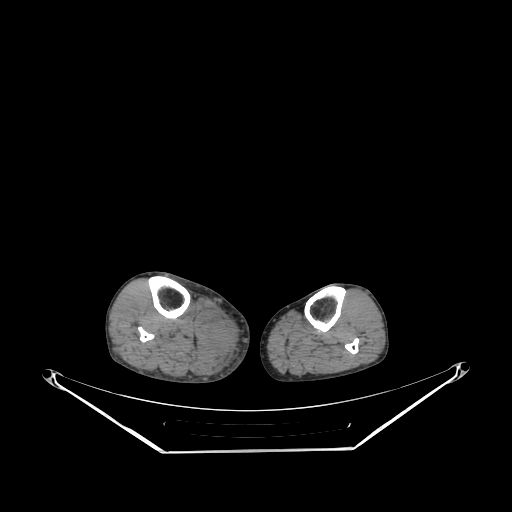
CT of an extremity soft-tissue mass (from a PET/CT study), one axial slice. Reconstruction kernel SOFT. 140 kVp. Soft-tissue window (W 400 / L 40 HU). 3.75 mm slice thickness. 512 × 512 image matrix, field of view 500 × 500 mm. Male patient. Case-level facts recorded for this patient, not image findings: histological type: pleiomorphic liposarcoma; grade: high; site of the primary tumour: right calf.
Structures marked on this image (expert contour drawn on MRI and transferred to this co-registered scan by the dataset authors):
- gross tumour volume including surrounding oedema: bounding box <201,311,236,355> (left, top, right, bottom; pixels)
- gross tumour volume (mass): <212,324,229,339>